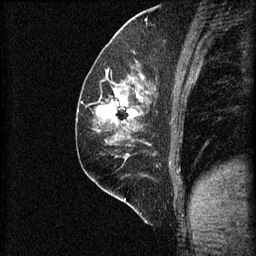
Breast MRI (dynamic contrast-enhanced), one sagittal slice. Position 31 of 60 along the scan axis. 3 images stored at this slice position (order not interpretable as contrast timing). 1.5 T. TE 4.2 ms, TR 8.2 ms. 2 mm slice thickness. 256 × 256 image matrix. Female patient, age 59 years.
Structures marked on this image (semi-automatic segmentation, software-assisted and operator-edited):
- analysis volume of interest (the breast-tissue region the enhancement analysis was run in; not a lesion): bounding box (x1, y1, x2, y2) in pixels: (93, 74, 155, 131)
- tumour enhancement mask (voxels above the 70 % enhancement threshold inside the analysis volume of interest): (98, 88, 144, 125)